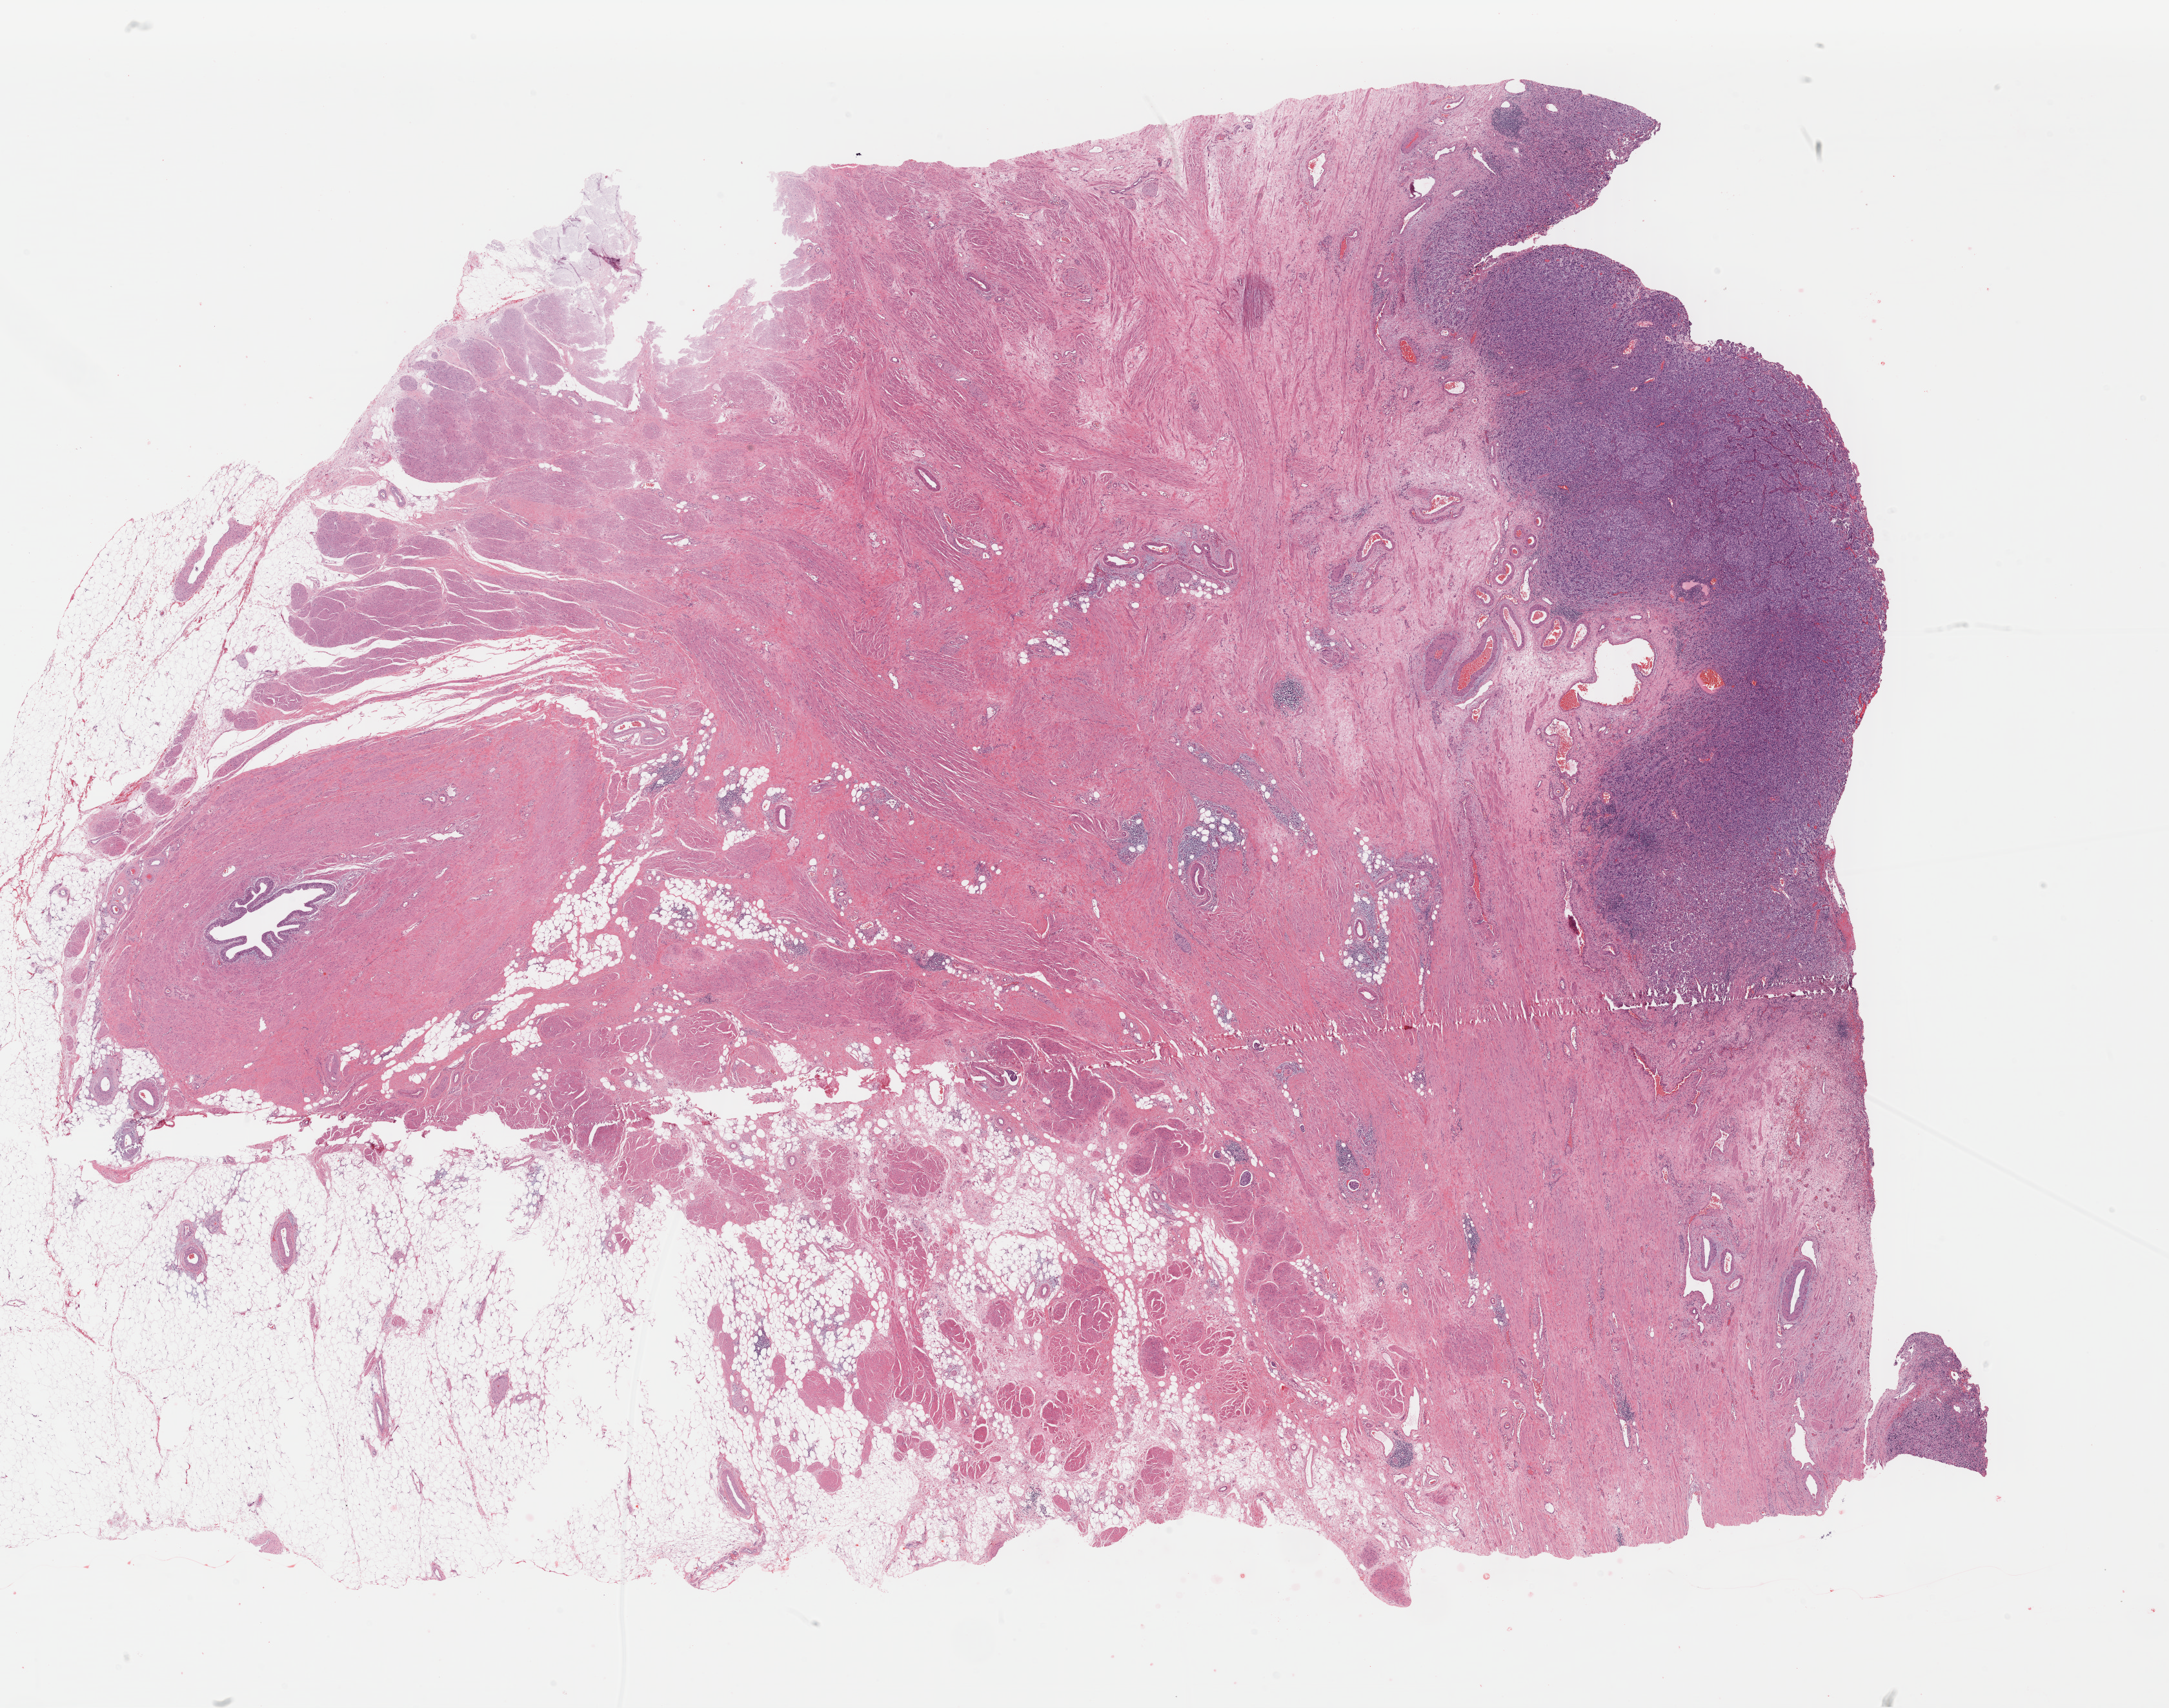
Whole-slide histology image, Hematoxylin and eosin (H&E) stained, whole scanned area (about 26.4 x 20.8 mm, from a 40x scan) shown as a low-resolution overview, formalin-fixed paraffin-embedded (FFPE) diagnostic section, bladder, primary tumour sample. Male, age 76 years at initial diagnosis. Histologic grade: high grade.
AJCC pathologic stage: IV (7th edition). Diagnosis: Transitional cell carcinoma. Lymph nodes positive (case pathology): 2 of 47 examined.